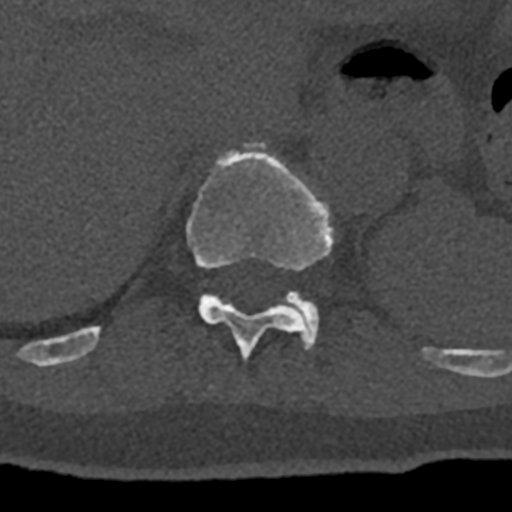
CT including the spine, one axial slice. Slice 539 of 797 in the series (ordered by position). Reconstruction kernel Br40s/3. Bone window (W 1800 / L 400 HU). 0.5 mm slice thickness. 512 × 512 image matrix, field of view 160 × 160 mm. Male patient, age 74 years. From the clinical record (not read from this slice): primary cancer: renal.
Annotated regions visible in this slice (semi-automatic segmentation, software-assisted and operator-edited):
- T11 vertebra: bounding box (x1, y1, x2, y2) in pixels: (70, 142, 432, 362)
- T12 vertebra: (284, 291, 319, 346)